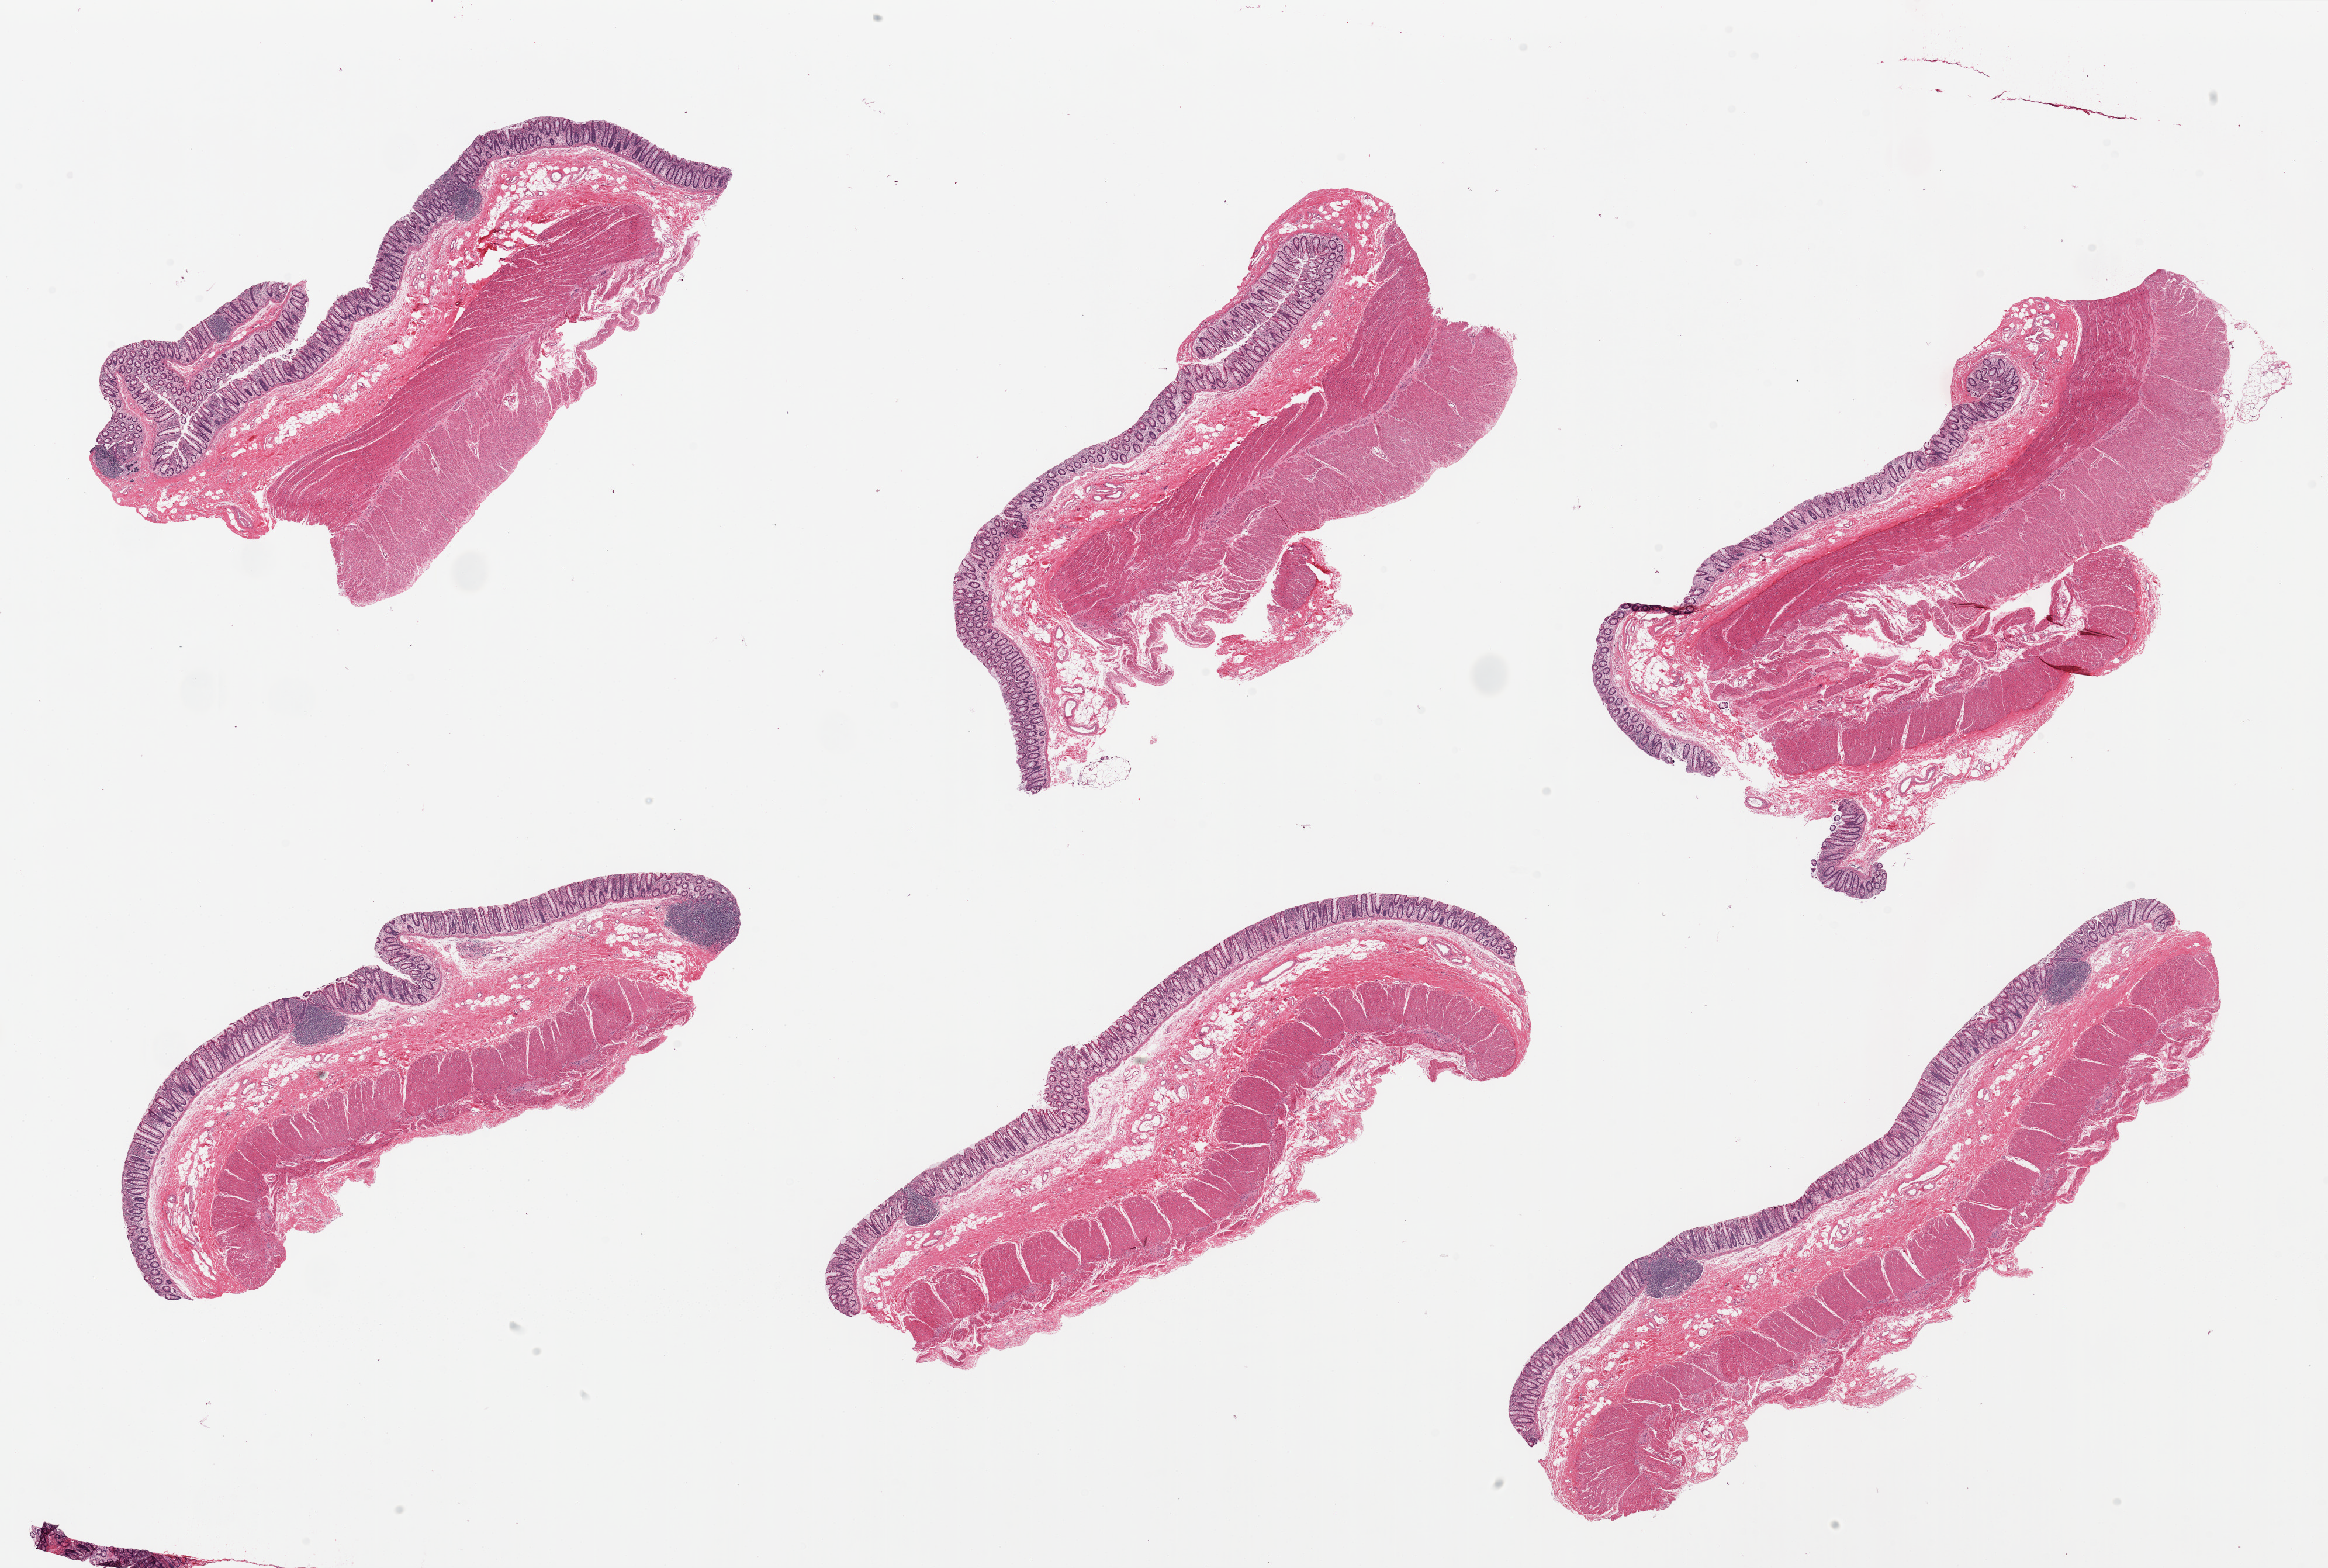
H&E whole-slide image, brightfield, low-resolution overview of the scanned area, about 31.5 x 21.2 mm. PAXgene-fixed paraffin-embedded (PFPE) section. Sampled site (target tissue): transverse colon. Donor tissue sample. Donor sex: male.
Reviewer comment on this tissue sample: 6 pieces, all with mucosa (2) and muscularis (1).